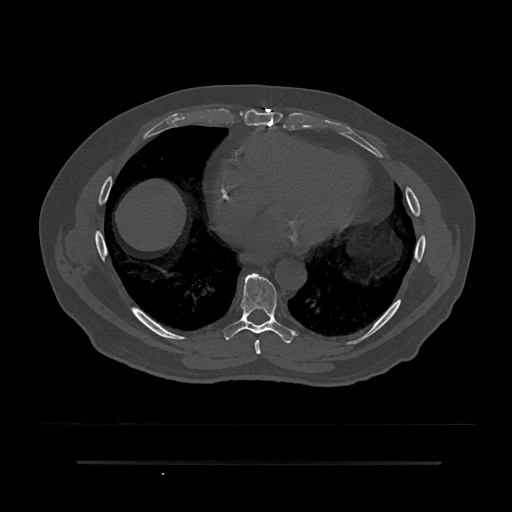
CT including the spine, one axial slice; position 434 of 797 along the scan axis; reconstruction kernel Br40s/3; 120 kVp; bone window (W 1800 / L 400 HU); 0.5 mm slice thickness; 512 × 512 image matrix. Patient: male, 59 years. Case-level facts recorded for this patient, not image findings: primary cancer: bile ducts; vertebrae with lytic lesions (as recorded): T10.
Structures marked on this image (semi-automatically segmented with operator editing):
- T7 vertebra: box from (x=255, y=340) to (x=261, y=354) px
- T8 vertebra: (x=223, y=273)–(x=295, y=343)